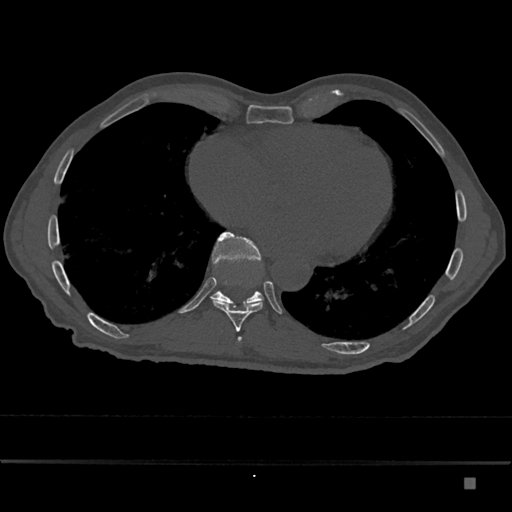
CT including the spine, one axial slice. Slice 782 of 797 in the series (ordered by position). 120 kVp. Bone window (W 1800 / L 400 HU). 0.5 mm slice thickness. 512 × 512 image matrix, field of view 390 × 390 mm. Patient: male, 72 years. Case-level facts recorded for this patient, not image findings: primary cancer: prostate.
Annotated regions visible in this slice (semi-automatic segmentation, software-assisted and operator-edited):
- T10 vertebra: box from (x=210, y=232) to (x=264, y=307) px
- T9 vertebra: (x=212, y=300)–(x=263, y=332)